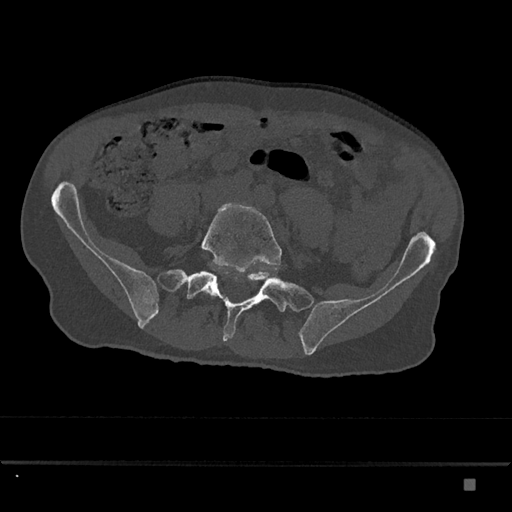
CT including the spine, one axial slice; slice 254 of 797 in the series (ordered by position); bone window (W 1800 / L 400 HU); 0.5 mm slice thickness; 512 × 512 image matrix. Male patient, age 72 years. Case-level facts recorded for this patient, not image findings: primary cancer: prostate.
Outlined on this slice (semi-automatically segmented with operator editing):
- L5 vertebra: bounding box [x1, y1, x2, y2] px = [201, 203, 282, 296]